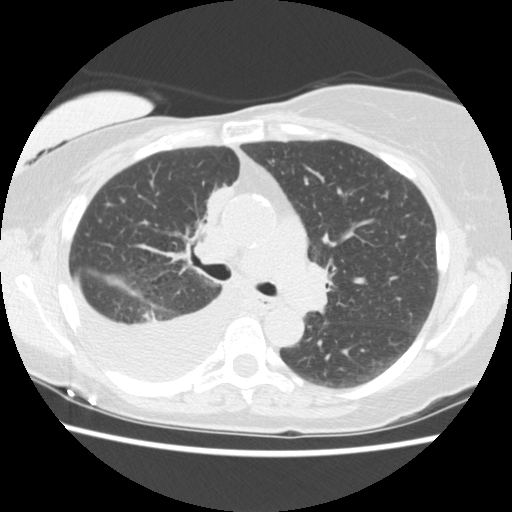
Chest CT (low-dose screening protocol), one axial image. Third screening round (two years after baseline). Lung window (W 1500 / L -600 HU). 2.5 mm slice thickness. Standard (soft-tissue) reconstruction kernel (STANDARD). 120 kVp. 512 × 512 image matrix, field of view 330 × 330 mm. Female, age 56 years at enrolment. Current smoker at enrolment.
Expert reader's lesion annotation, bounding box <183,178,245,244> (left, top, right, bottom; pixels). The screening reader recorded 2 non-calcified nodules or masses ≥4 mm on this exam; which of them this box marks is not recorded. Official screen result: positive, other.